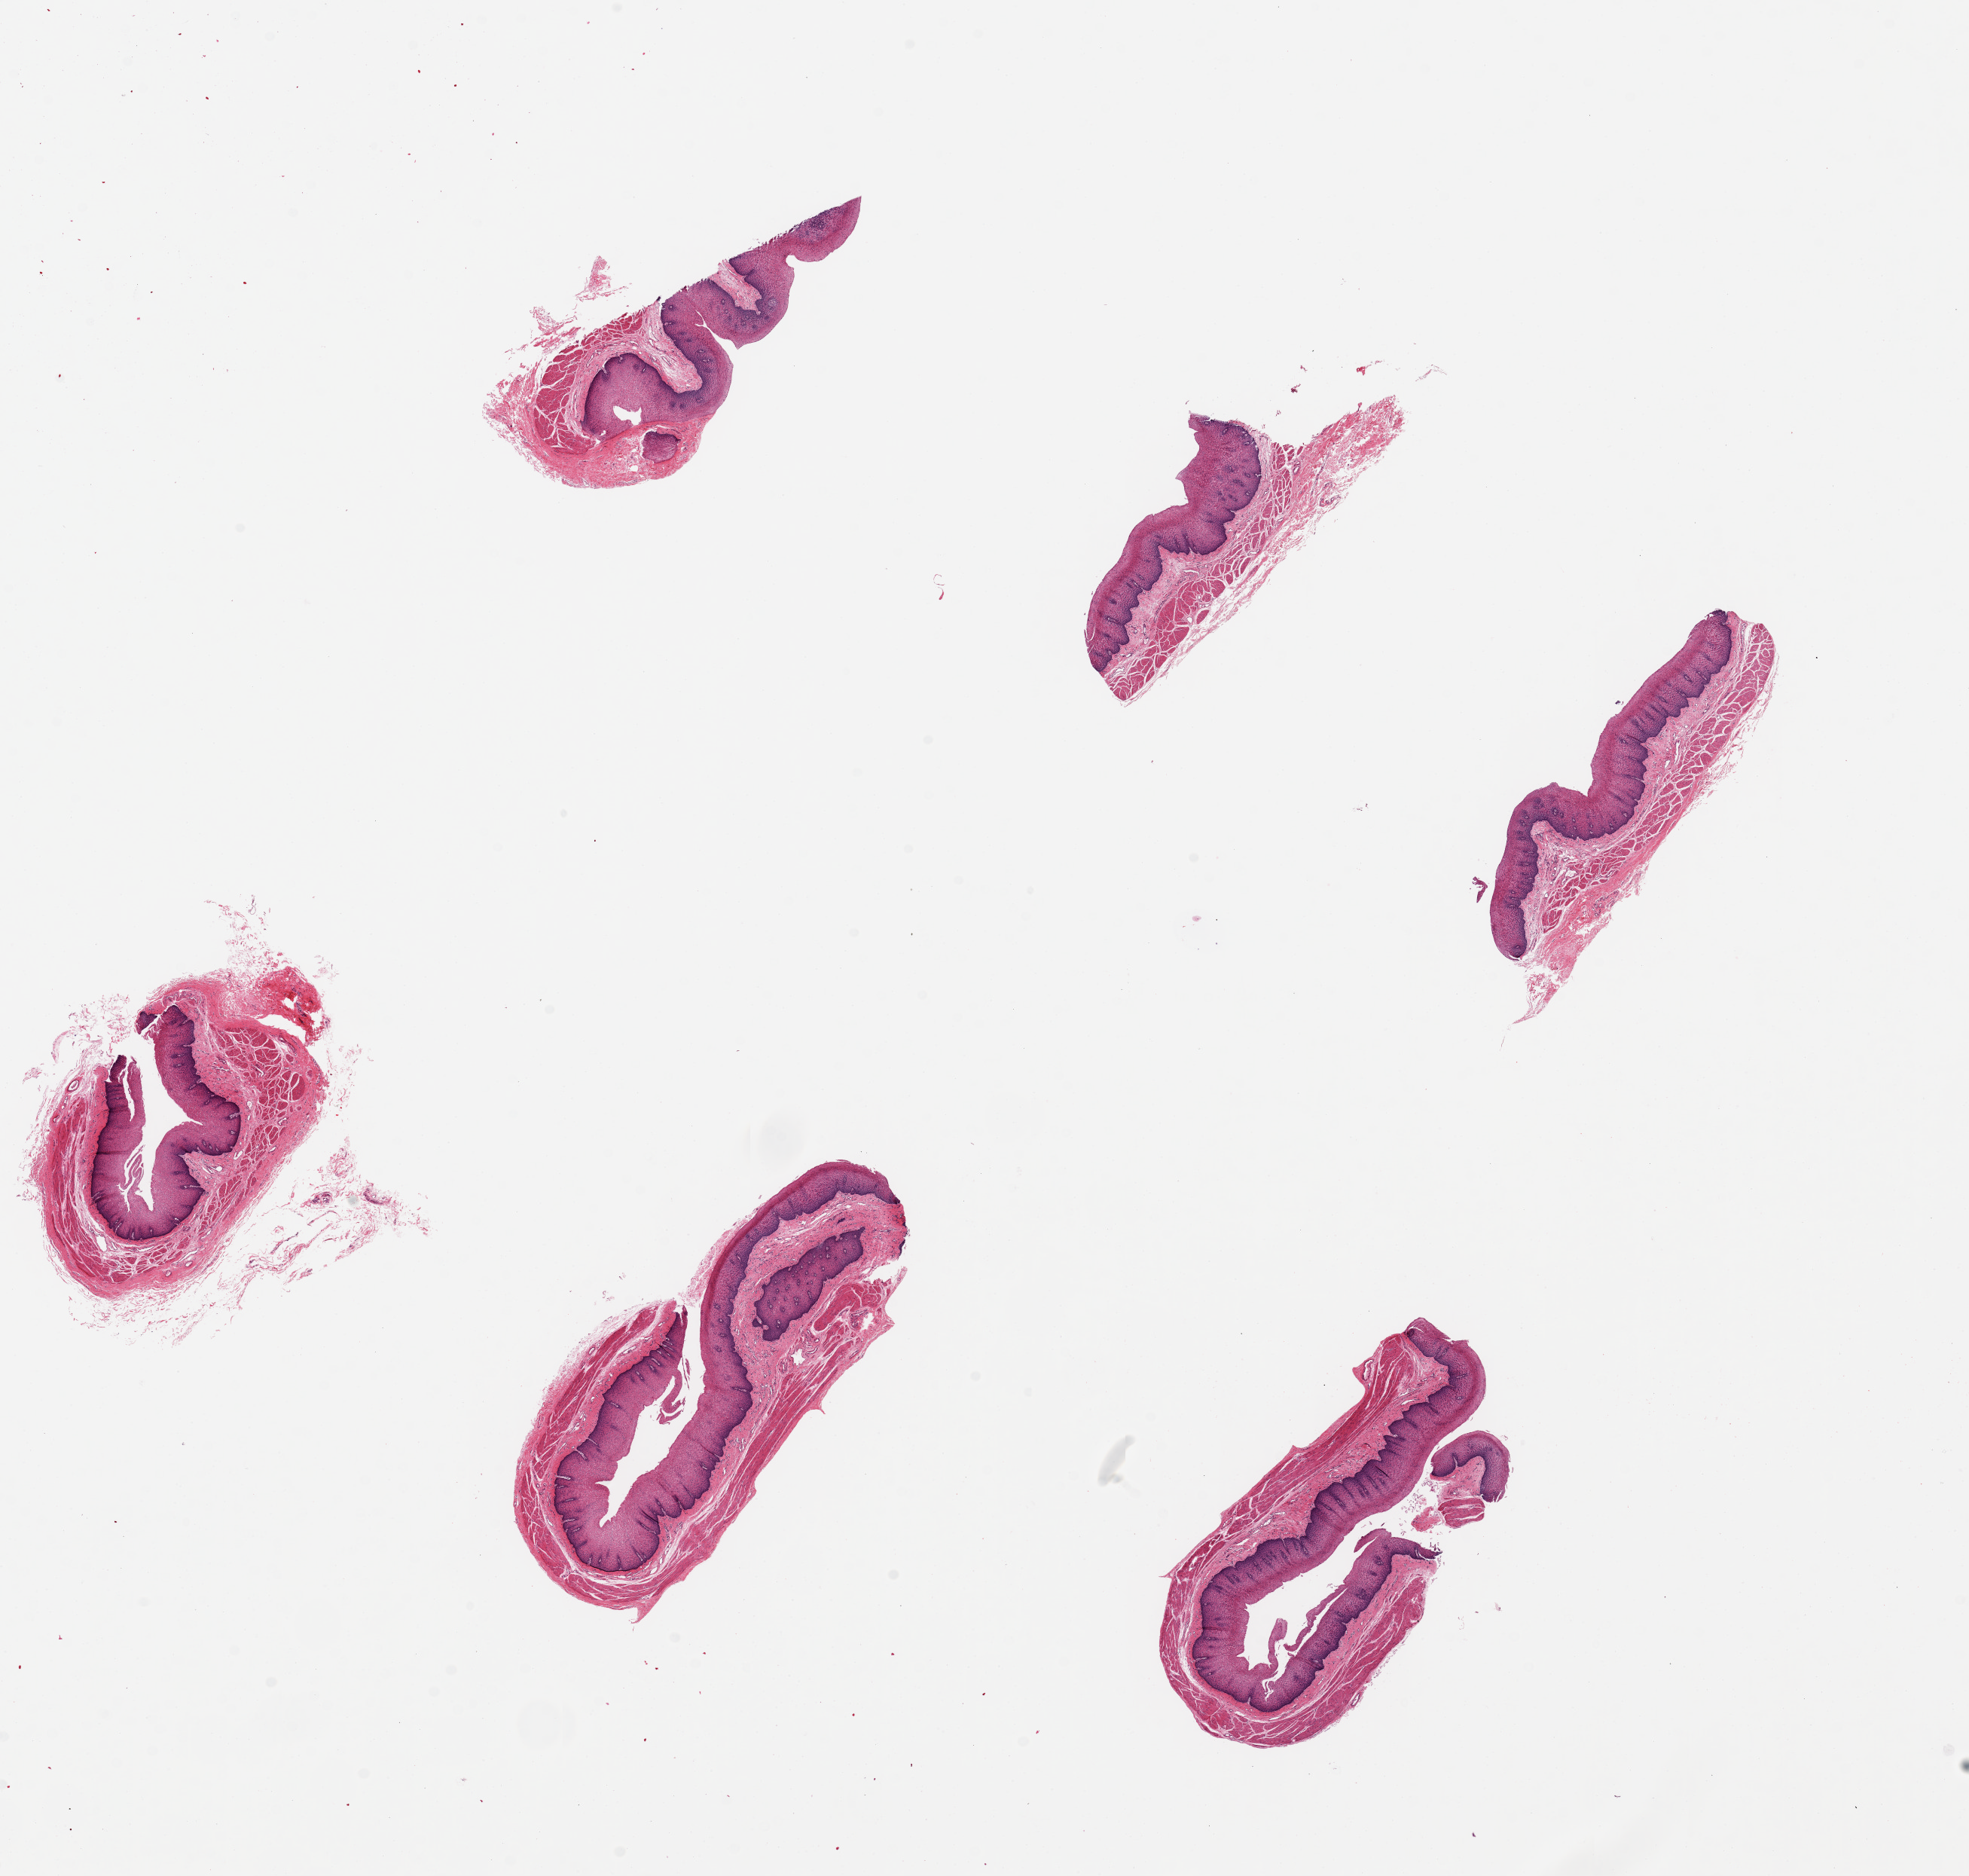
Whole-slide image, haematoxylin and eosin stain, shown as a low-resolution overview of the whole scanned area (about 20.7 x 19.7 mm, slide scanned at 20x). PAXgene-fixed, paraffin-embedded tissue. Section of esophageal mucous membrane (target tissue). Tissue donor sample. Donor: female.
• reviewer comment on this tissue sample: 6 pieces, up to 5x2mm; ~25%-50% thicknes is squamous mucosa, well preserved